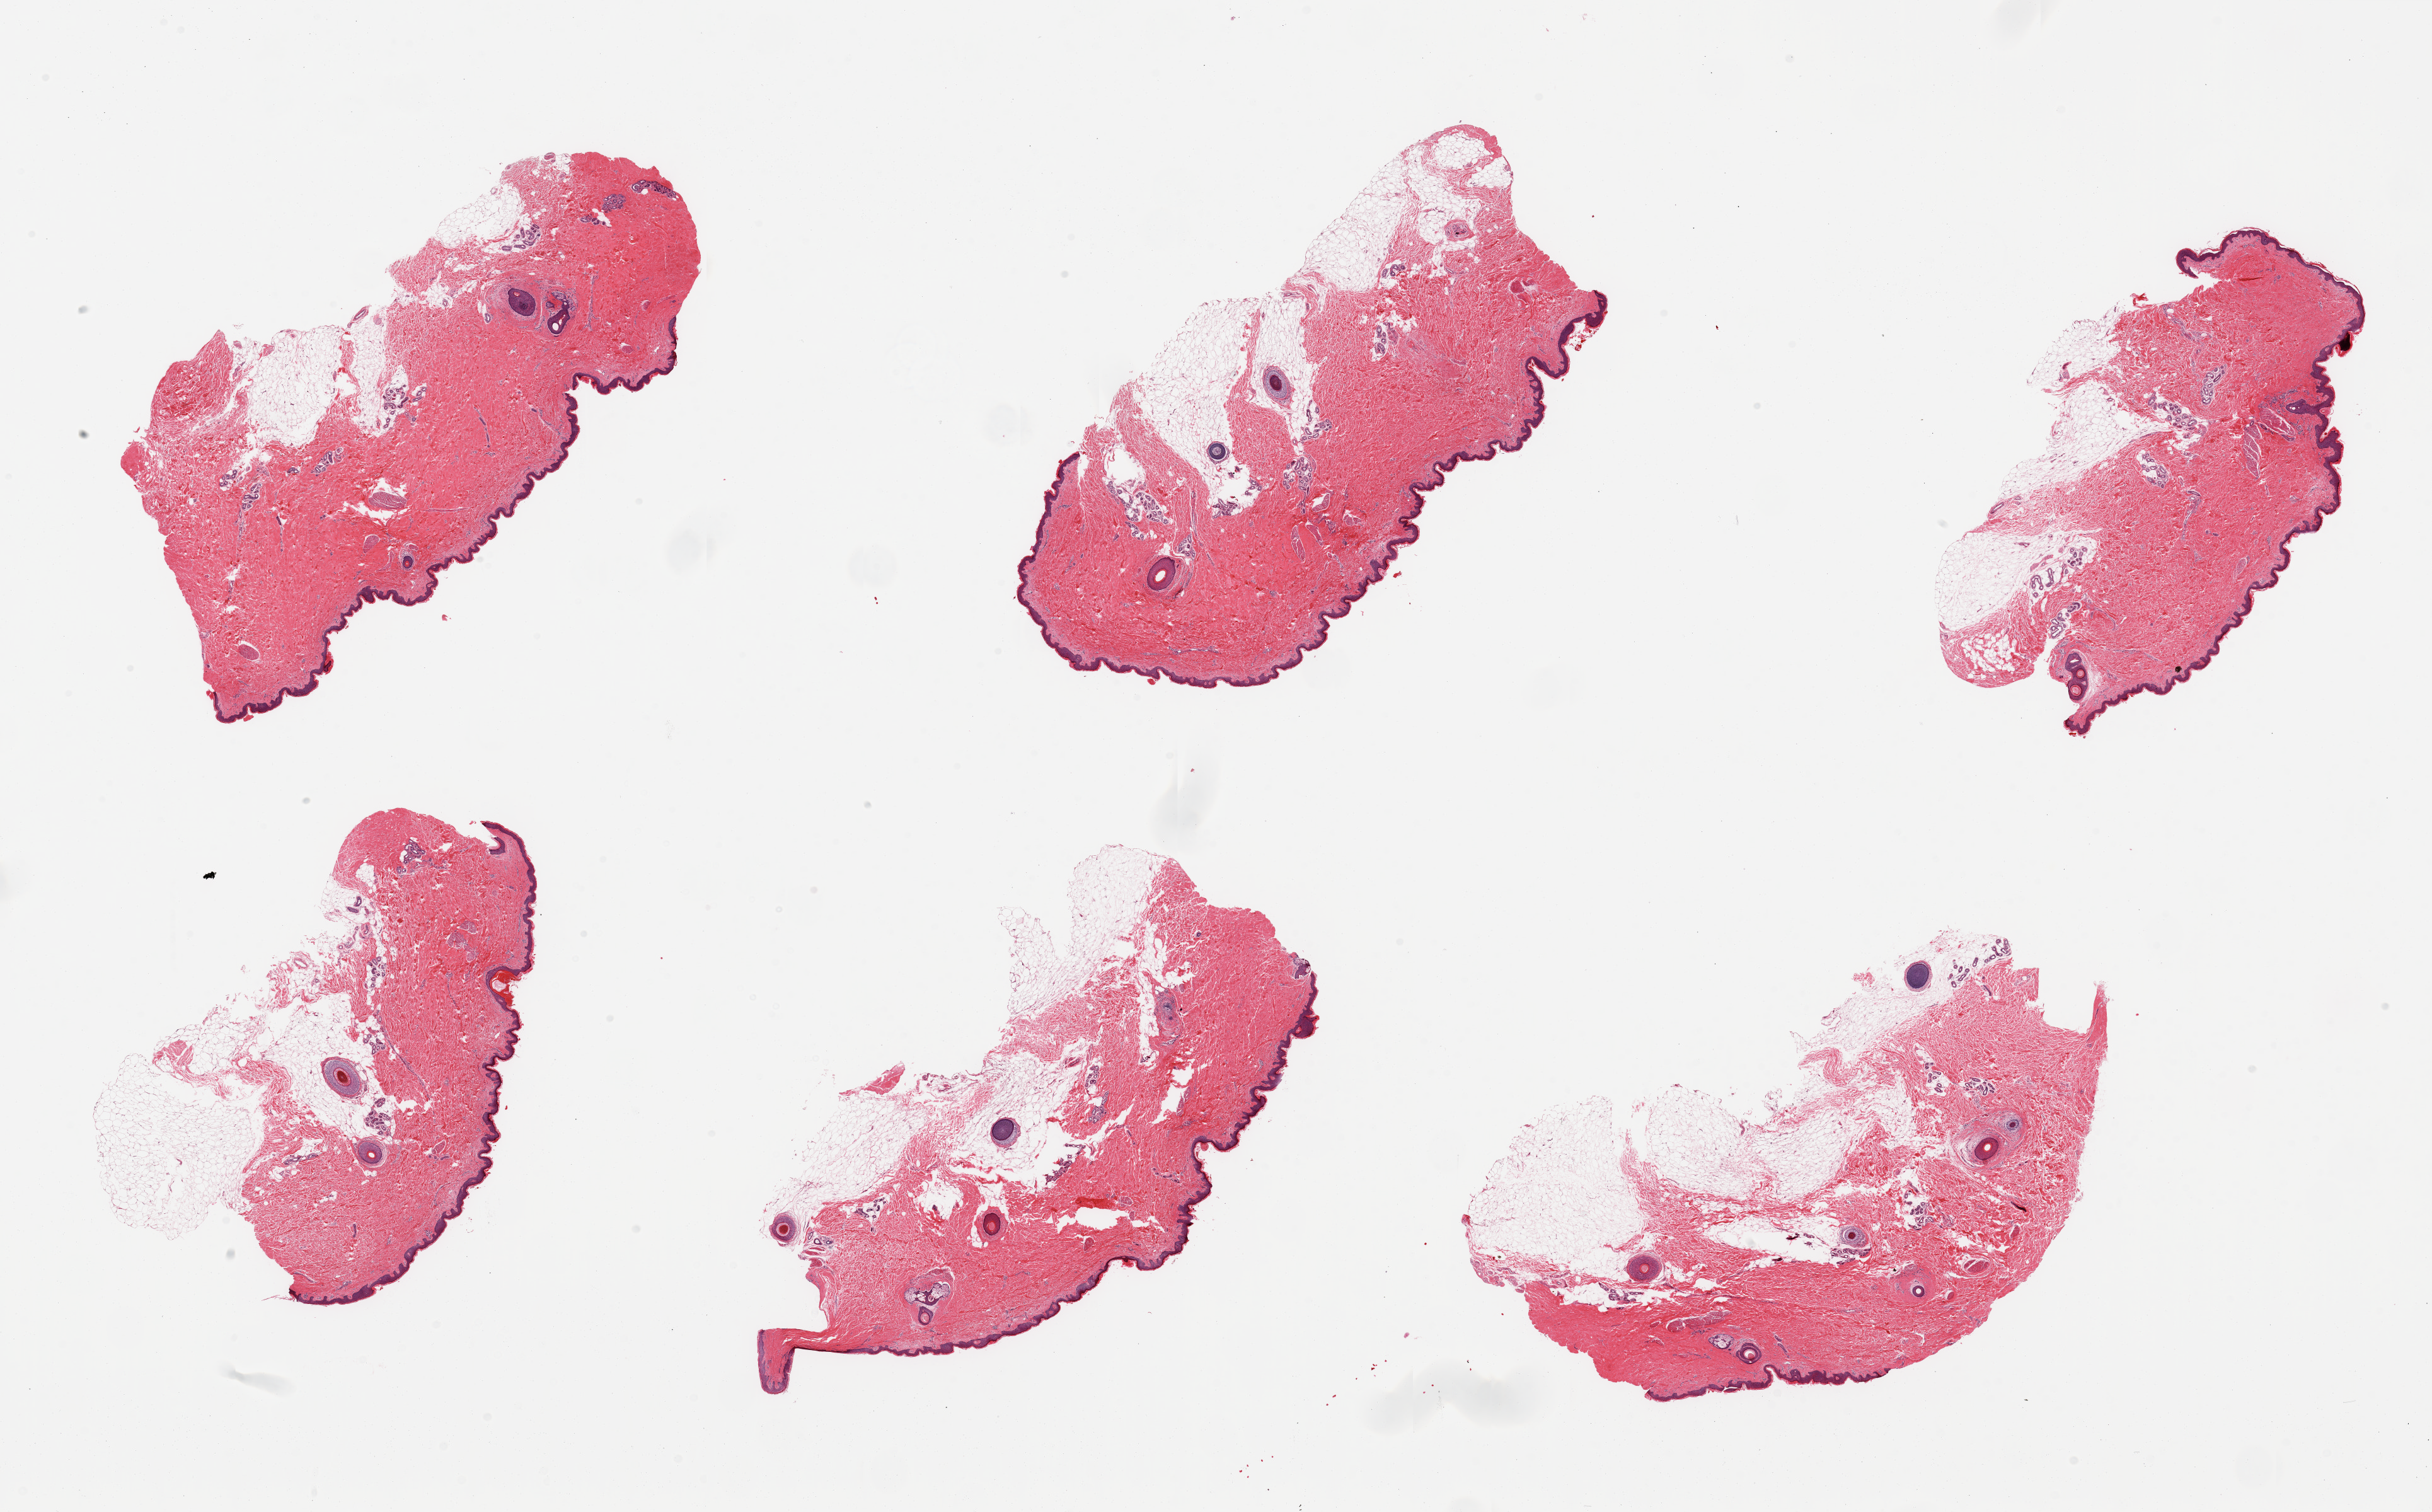
Digitized H&E-stained section, brightfield, whole scanned area (about 30.5 x 19.0 mm, slide scanned at 20x) shown as a low-resolution overview; PAXgene-fixed, paraffin-embedded tissue; target tissue: skin of suprapubic region; tissue donor sample. Donor: male.
• review note (as recorded): 6 pieces; each piece contains up to 30% of mainly subcutaneous fat